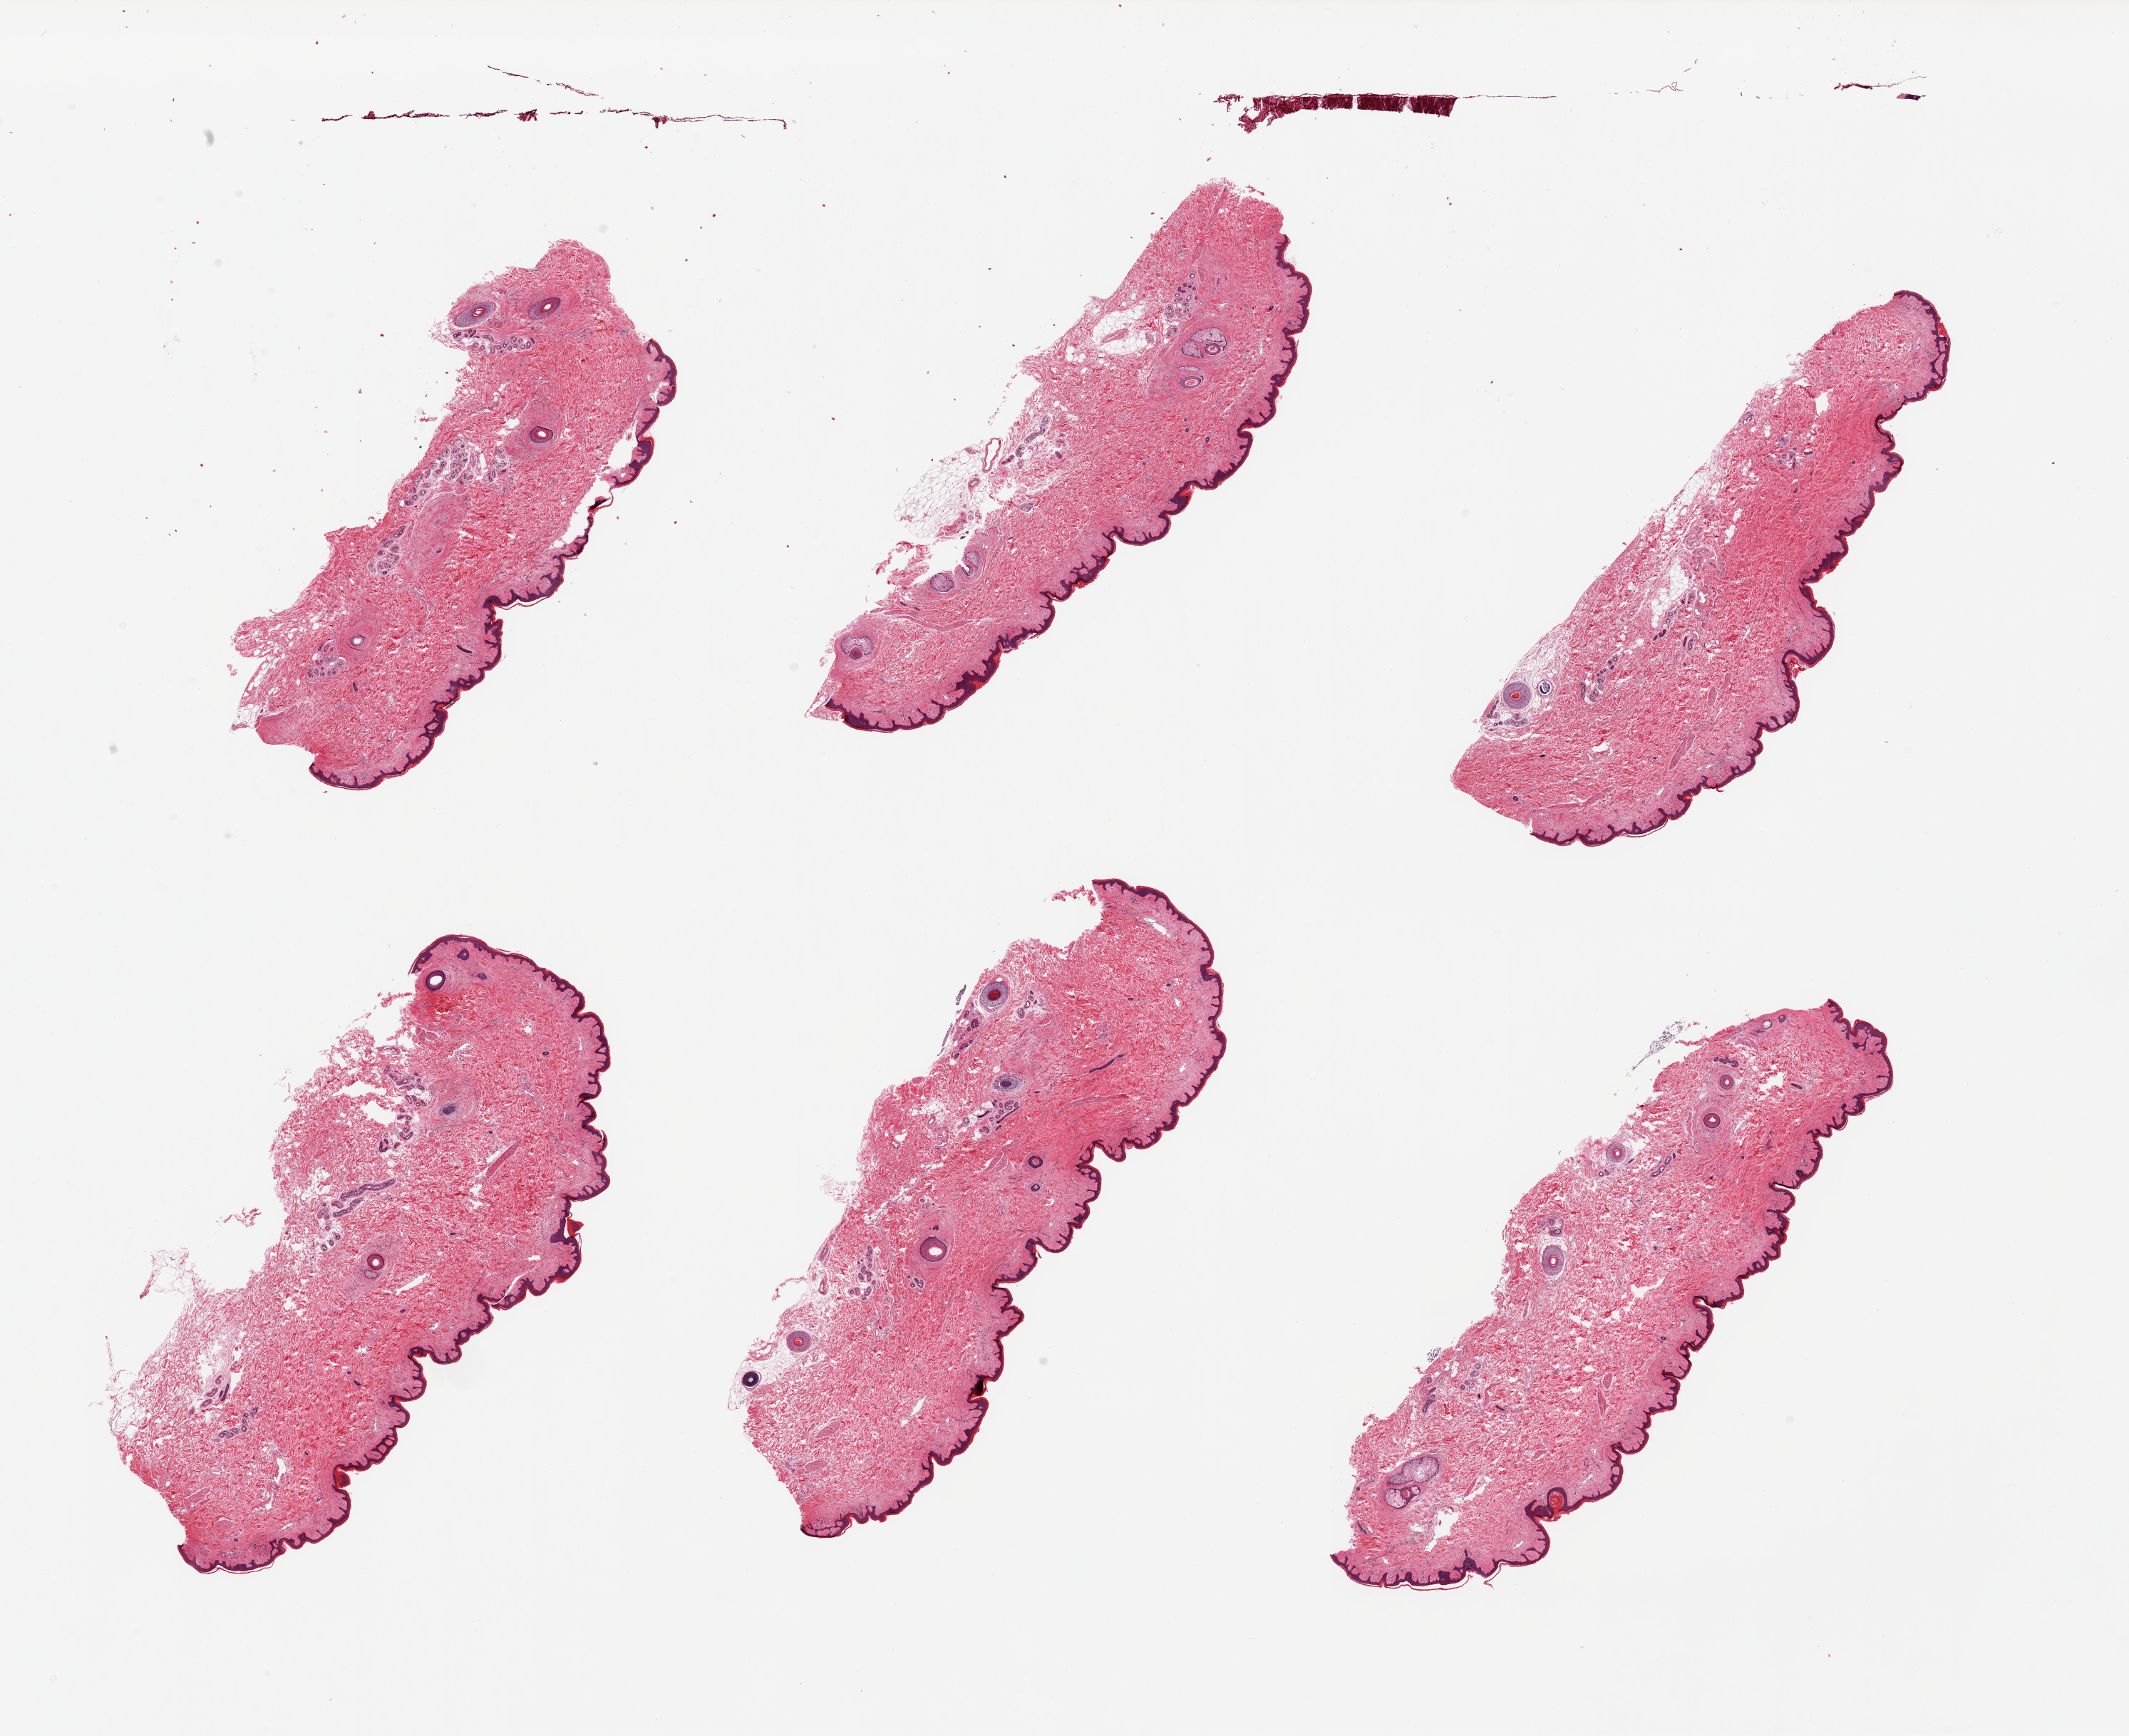
Whole-slide image, H&E stain, a low-resolution overview of the entire scanned area, about 23.6 x 19.3 mm, PAXgene-fixed paraffin-embedded (PFPE) section, section of skin of suprapubic region (target tissue), tissue donor sample. Donor sex: female.
Review note (as recorded): 6 pieces; hair bearing skin and ~5% periadnexal fat; epidermis is ~33 microns.